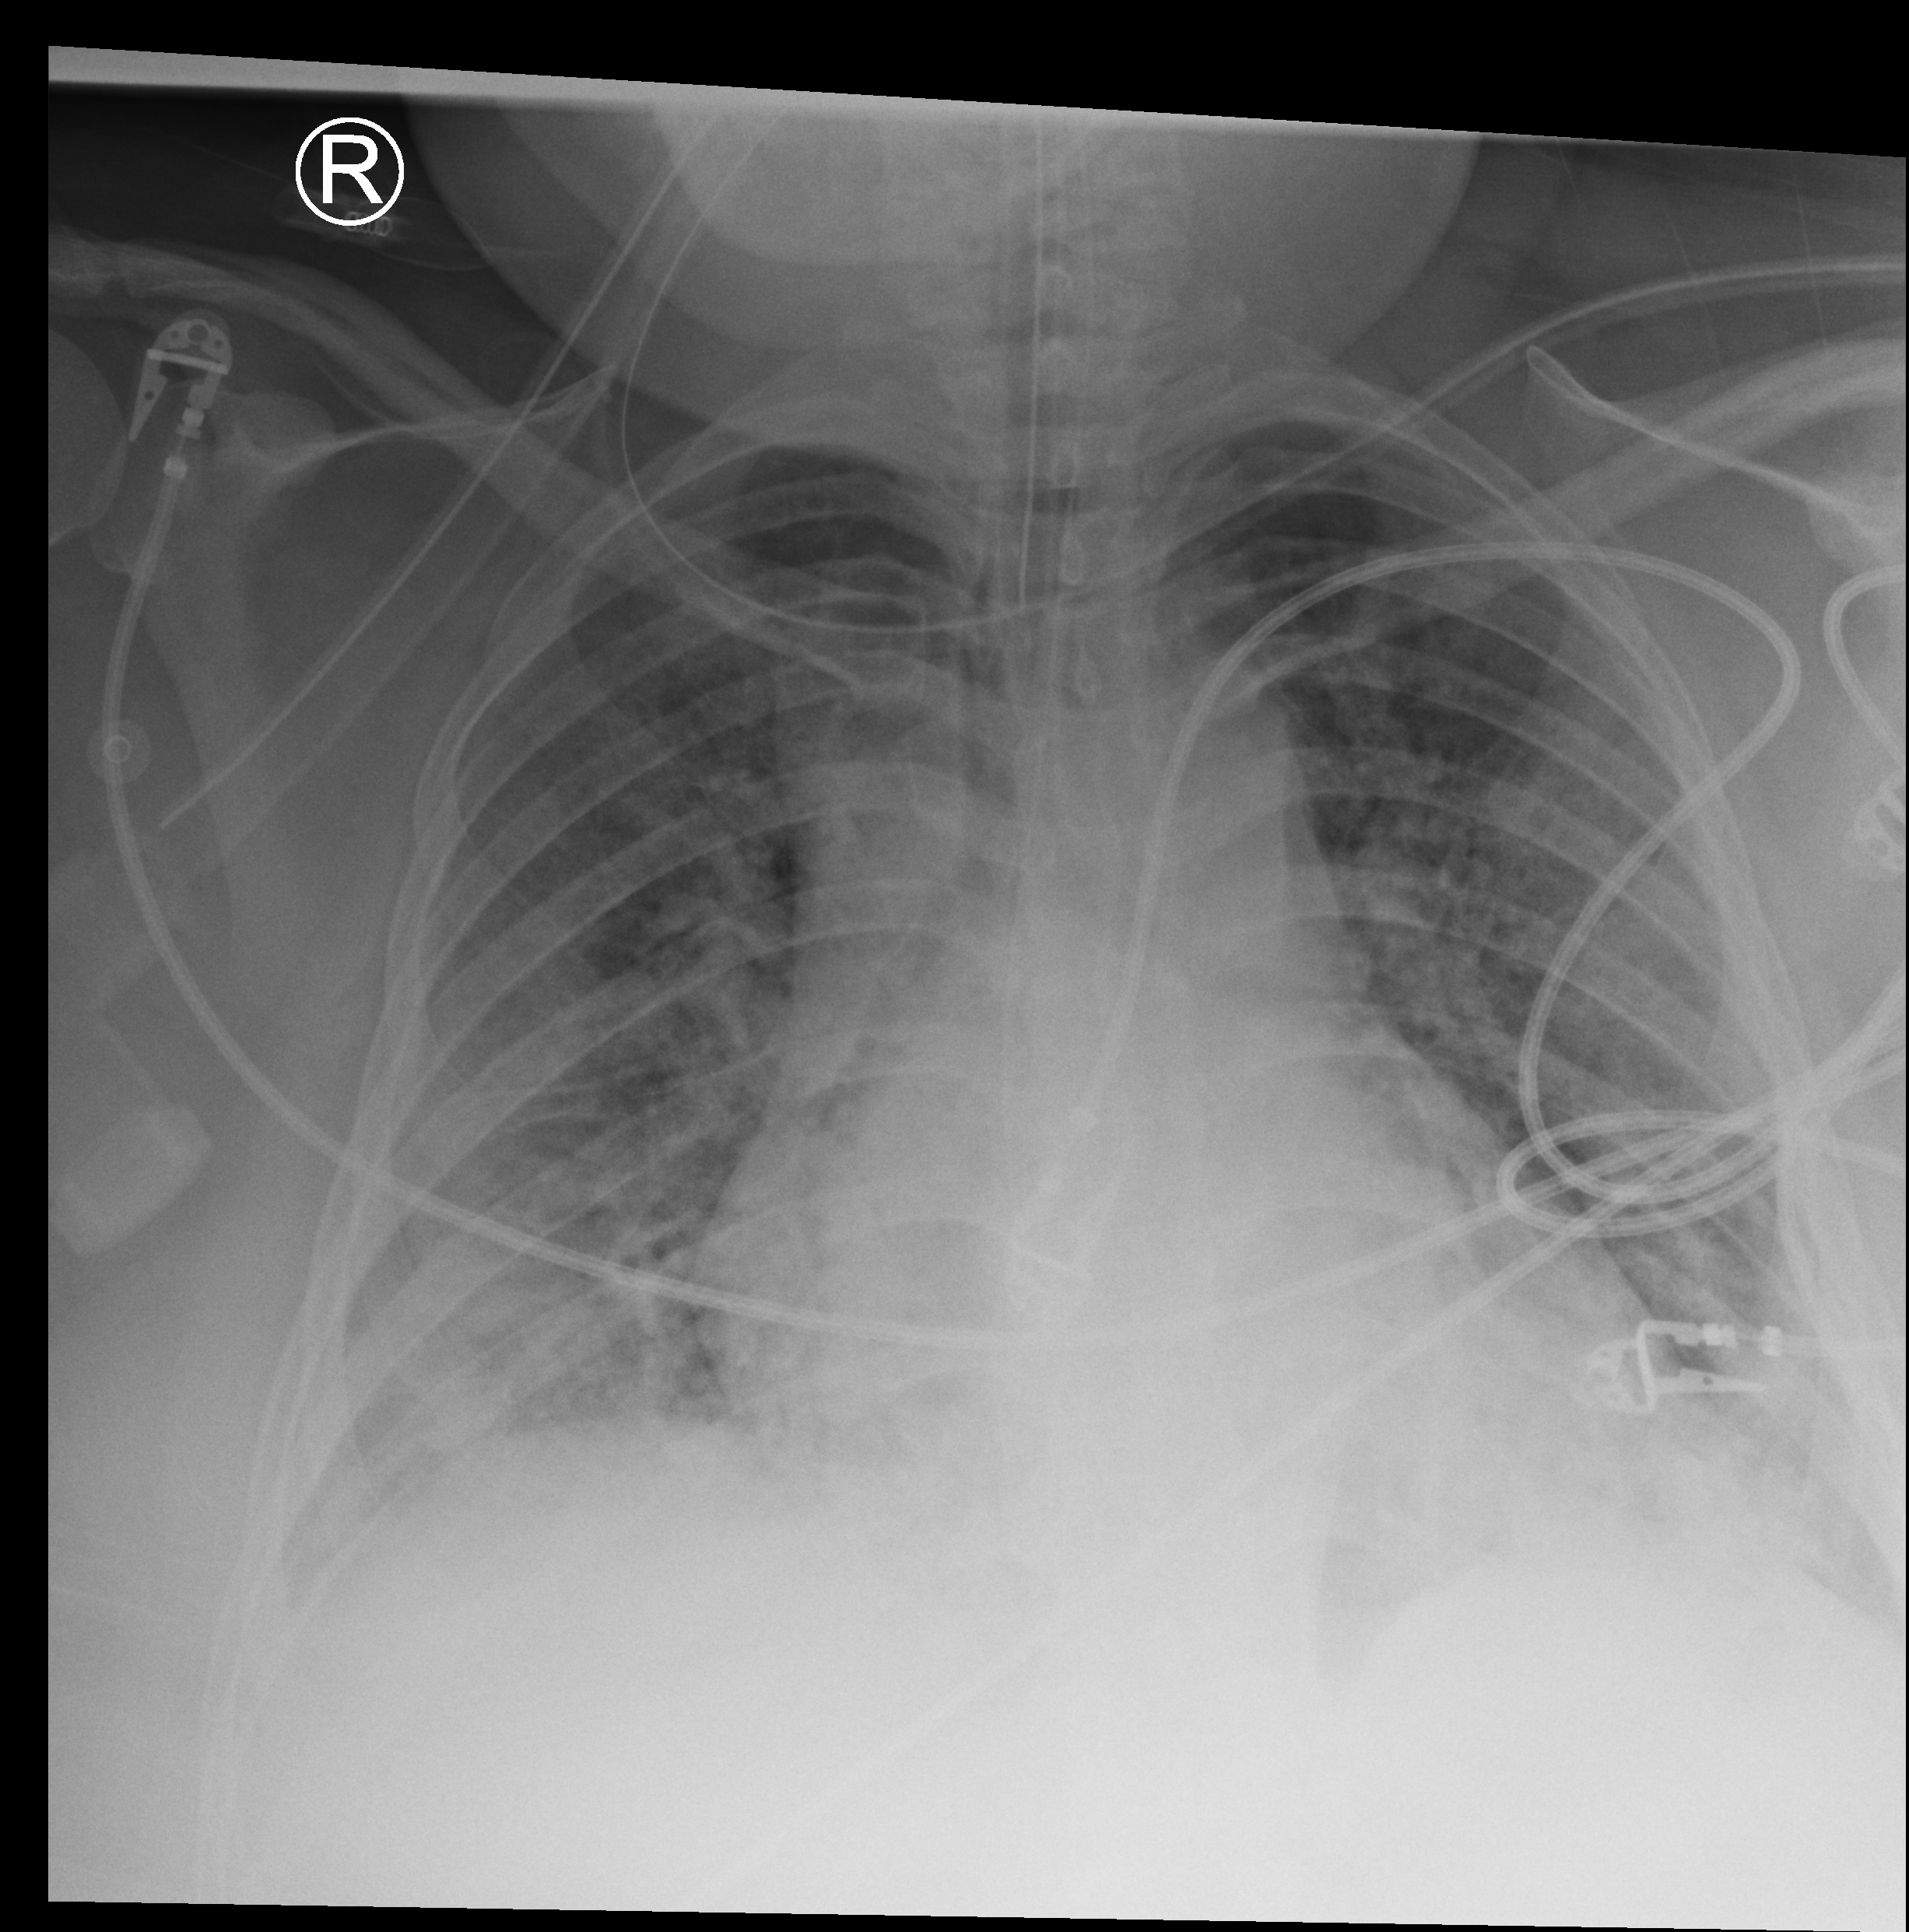
Portable chest radiograph, anteroposterior (AP) projection. Female patient hospitalised with COVID-19, age 18–59 years.
Hospital-stay facts (about this admission, not read from this image; timing relative to this image not recorded): diabetes (admission record): yes.